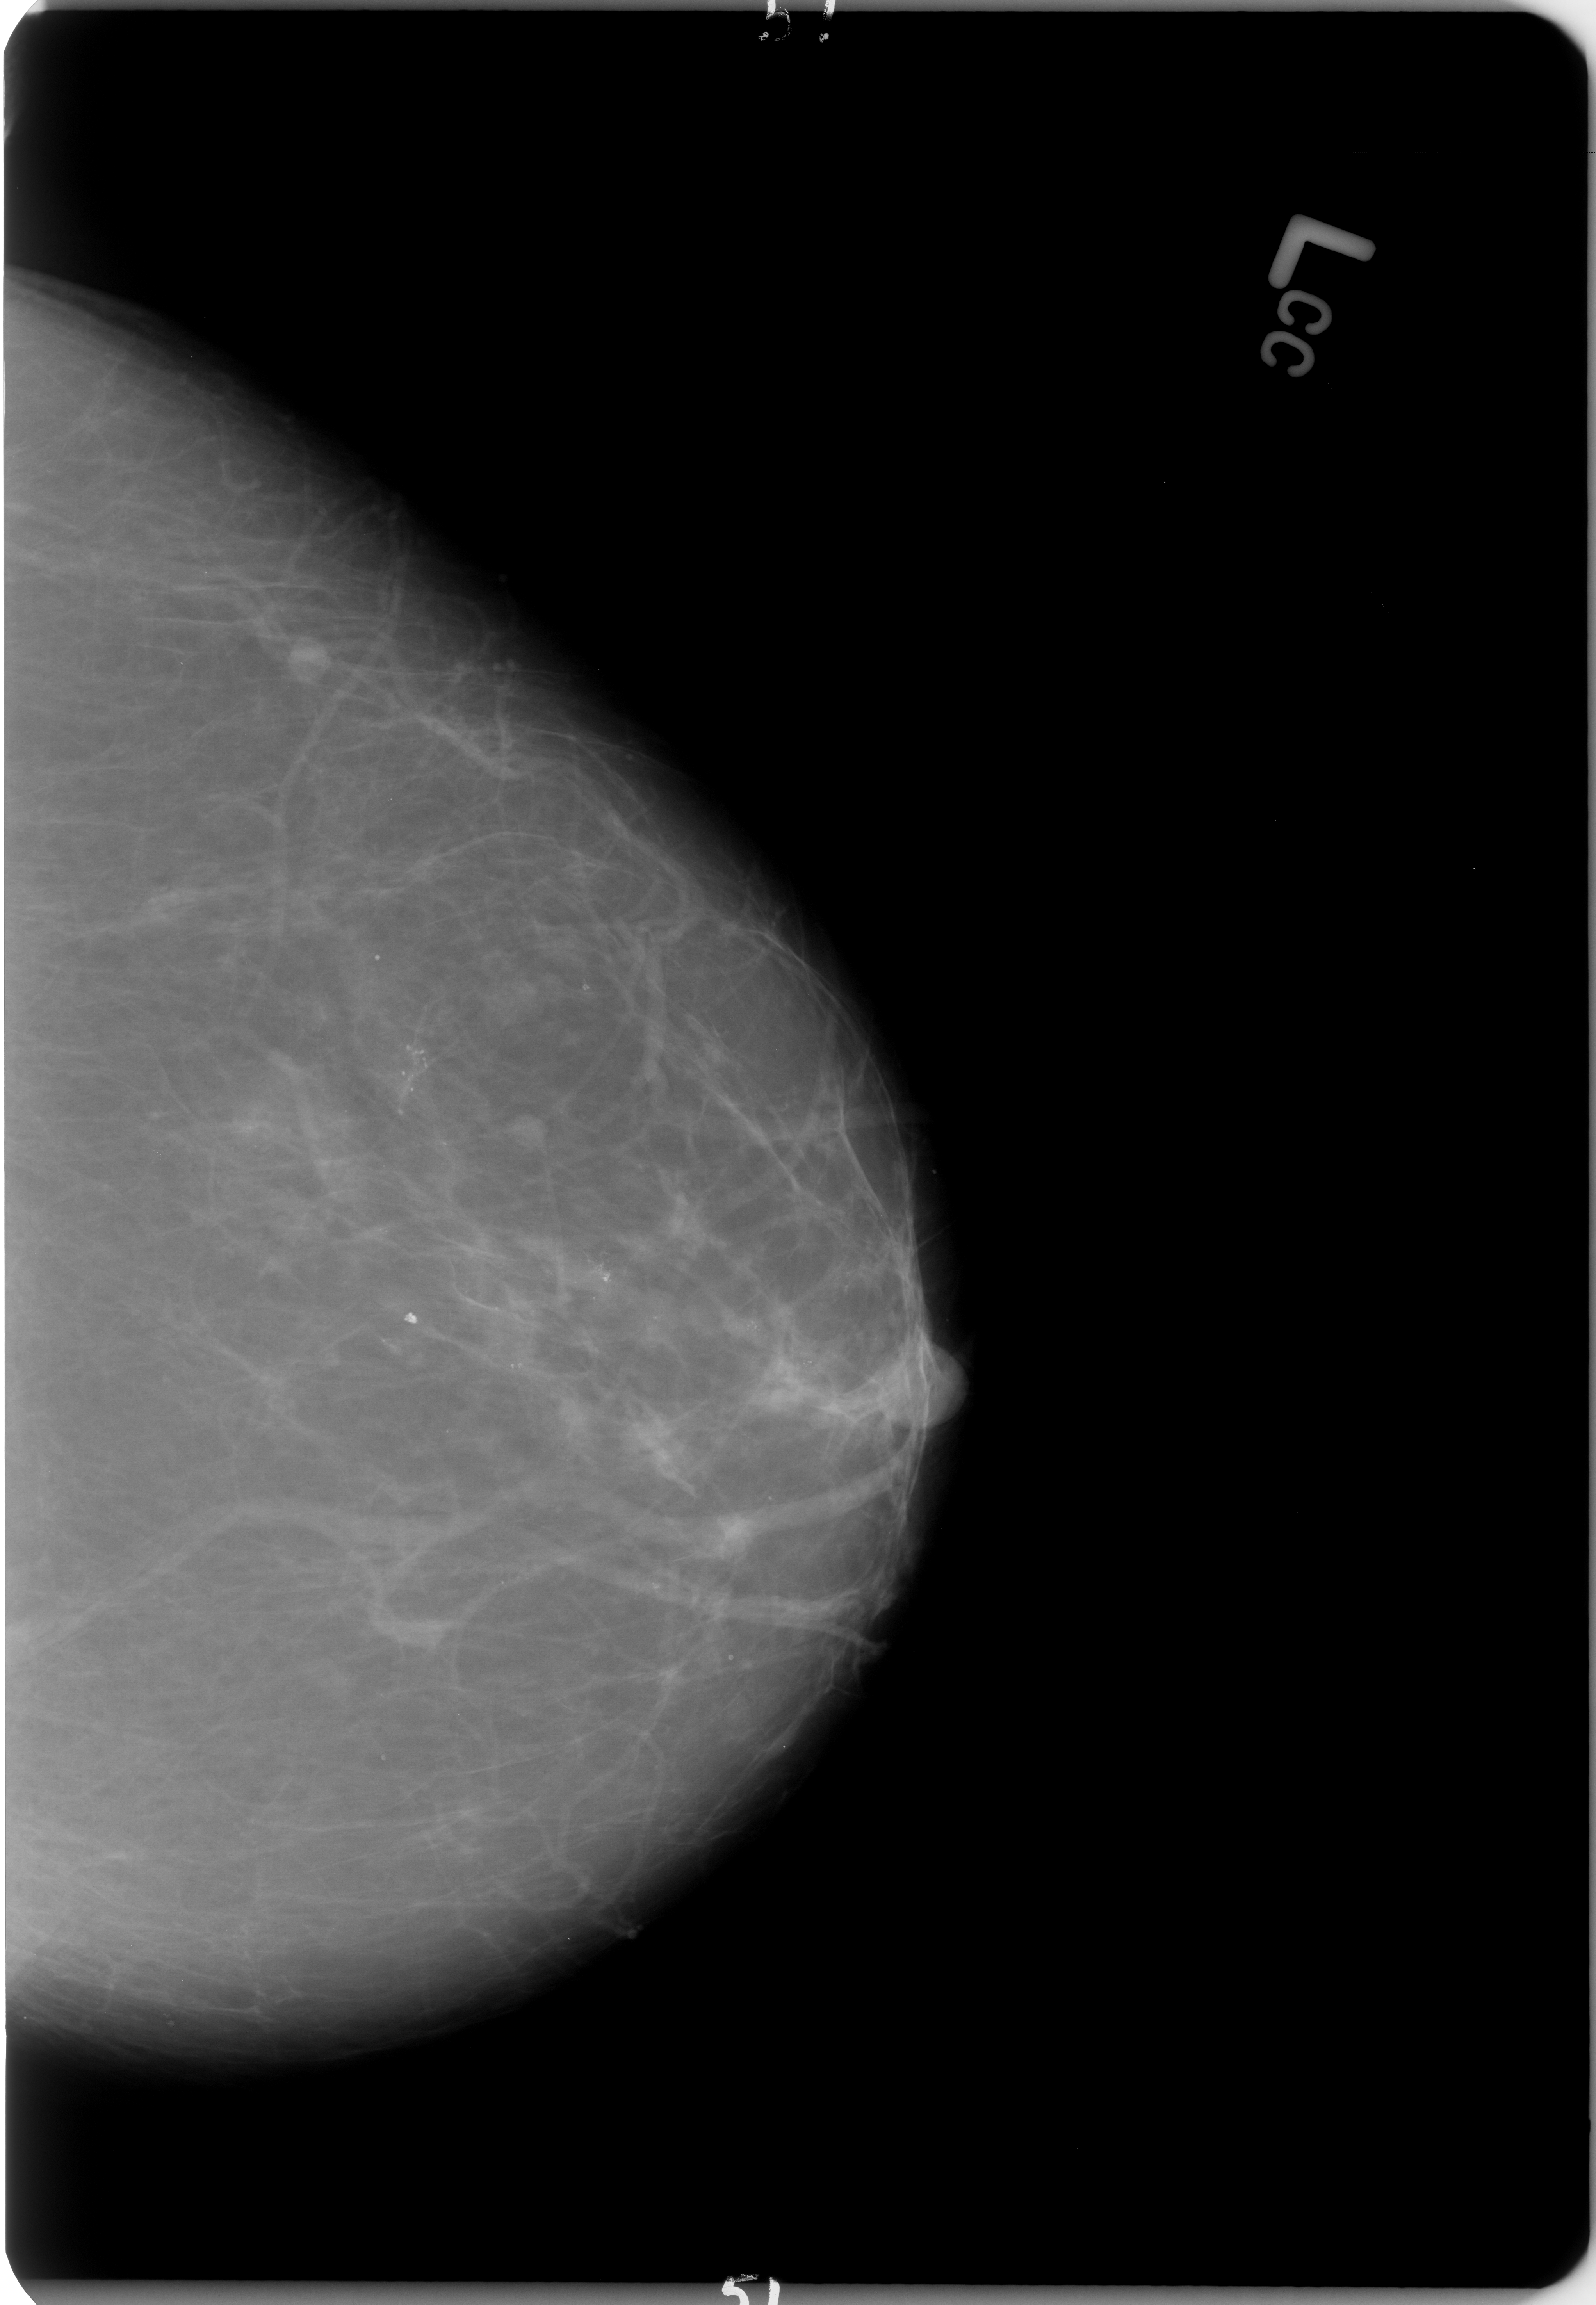
Mammogram (digitized film); left breast; craniocaudal (CC) view; breast composition: scattered fibroglandular densities (BI-RADS density category 2 of 4); 1596 × 2305 image matrix.
Expert-marked regions of interest on this film, with their recorded descriptors:
- Finding 1 of 2: calcifications, morphology pleomorphic / pleomorphic, distribution regional / regional; BI-RADS assessment category 4; pathology result (as recorded, not read from the image): benign: bounding box [x1, y1, x2, y2] px = [371, 1021, 460, 1135]
- Finding 2 of 2: calcifications, morphology pleomorphic, distribution regional; BI-RADS assessment category 4; subtlety rating 4 on a 1 (subtle) to 5 (obvious) scale; pathology (as recorded): benign: [584, 1239, 641, 1306]